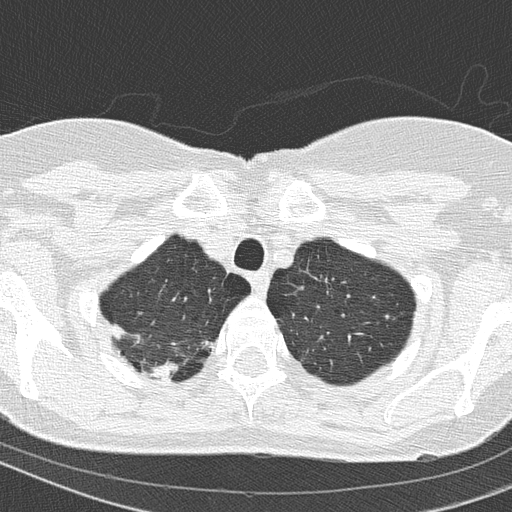
Low-dose screening chest CT, one axial slice. Position 135 of 154 along the scan axis. Reconstruction kernel B50f. 120 kVp. Lung window (W 1500 / L -600 HU). 2 mm slice thickness. 512 × 512 image matrix.
Structures marked on this image (outlined manually by an expert reader):
- lesion 1 (tumor, upper lobe of right lung): bounding box (x1, y1, x2, y2) in pixels: (142, 360, 178, 382)